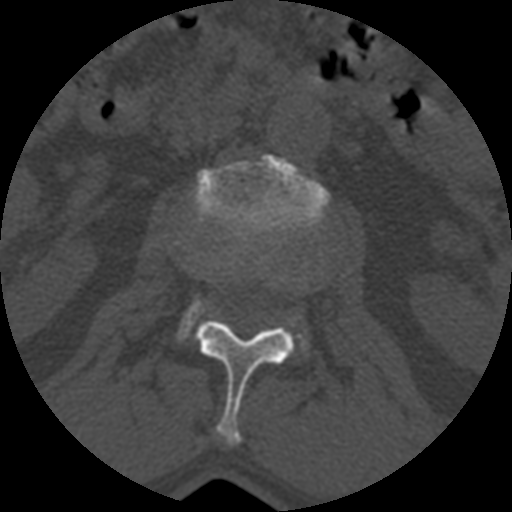
CT including the spine, one axial slice. Position 350 of 399 along the scan axis. Reconstruction kernel STANDARD. 120 kVp. Bone window (W 1800 / L 400 HU). 1.25 mm slice thickness. 512 × 512 image matrix, field of view 160 × 160 mm. Patient age 71 years. Case-level facts recorded for this patient, not image findings: primary cancer: prostate.
Annotated regions visible in this slice (semi-automatic segmentation, software-assisted and operator-edited):
- L1 vertebra: bounding box (x1, y1, x2, y2) in pixels: (196, 319, 293, 444)
- L2 vertebra: (175, 155, 329, 353)